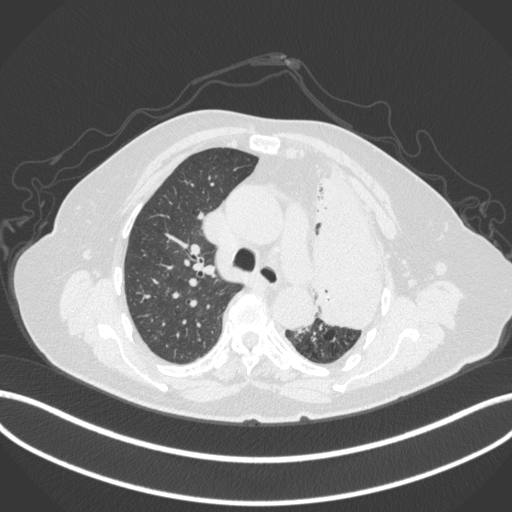
Chest CT, one axial slice. Slice 271 of 399 in the series (ordered by position). 120 kVp. Lung window (W 1500 / L -600 HU). 1 mm slice thickness. 512 × 512 image matrix, field of view 400 × 400 mm. Female patient, age 75 years. From the clinical record (not read from this slice): clinical TNM (as recorded): T3 N3 M1.
Annotated regions visible in this slice (rectangle marked by the reading radiologist):
- lung tumour (recorded histology: adenocarcinoma): box from (x=314, y=160) to (x=391, y=334) px